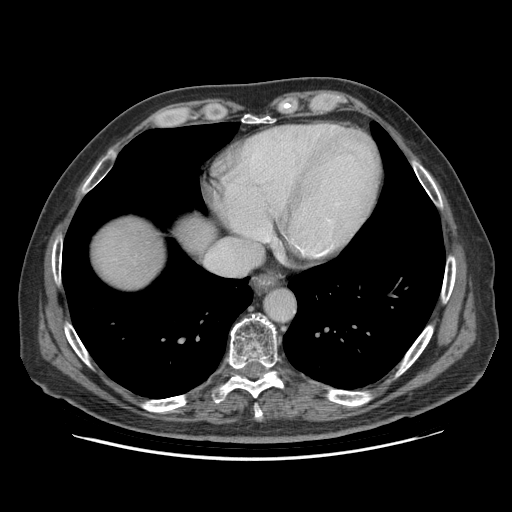
Contrast-enhanced abdominal CT (liver protocol), one axial slice. Slice 83 of 95 in the series (ordered by position). Reconstruction kernel STANDARD. 140 kVp. Soft-tissue window (W 400 / L 40 HU). 2.5 mm slice thickness. 512 × 512 image matrix, field of view 400 × 400 mm. Case-level facts recorded for this patient, not image findings: diagnosis: hepatocellular carcinoma (patient treated with transarterial chemoembolisation; whether this scan precedes or follows treatment is not stated here); TNM stage (as recorded): Stage-IVB; Child-Pugh class: A; tumour differentiation: well differentiated; tumour nodularity: uninodular.
Outlined on this slice (semi-automatic segmentation, software-assisted and operator-edited):
- liver parenchyma outside the tumour (the mass and vessels are separate outlines, so this box may not span the whole liver): bounding box [x1, y1, x2, y2] px = [96, 218, 164, 288]